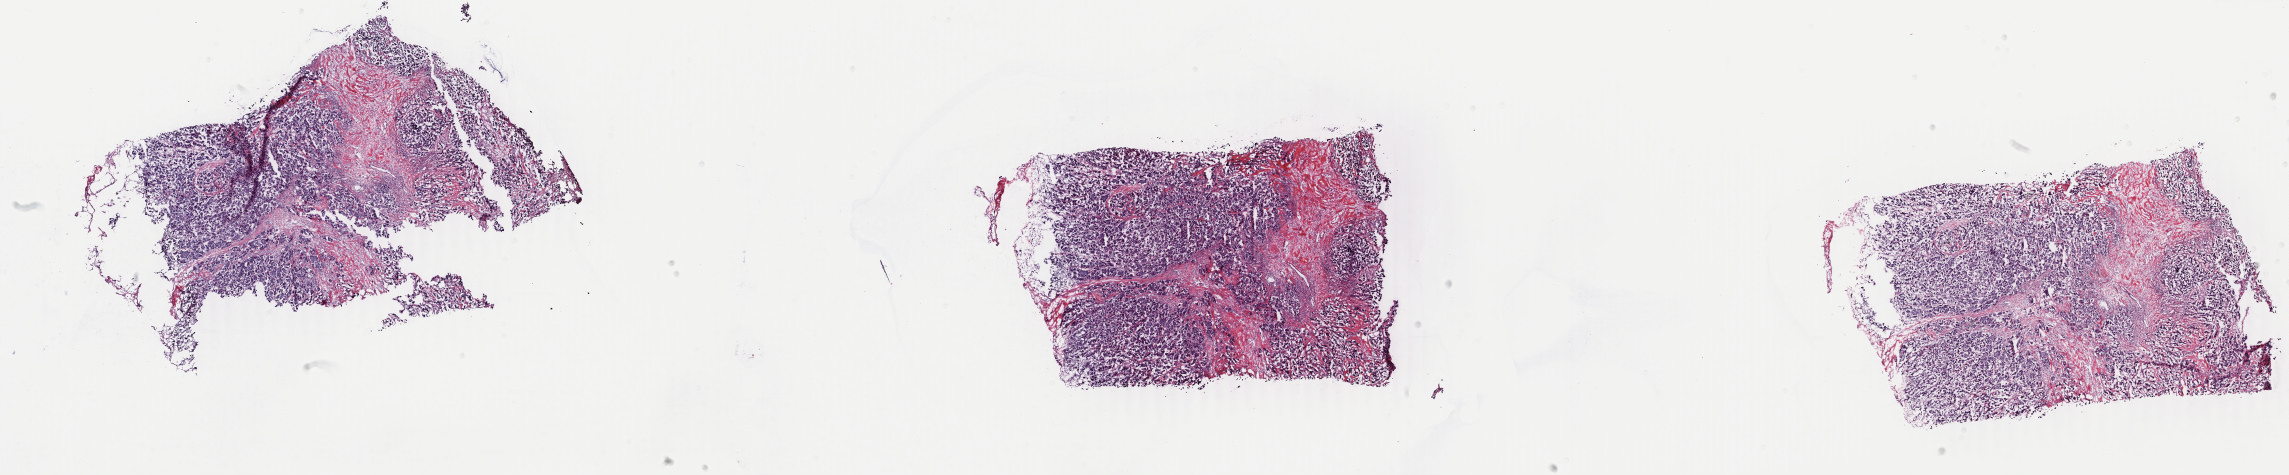
Hematoxylin and eosin (H&E) stained whole-slide image — shown as a low-resolution overview of the whole scanned area (about 36.4 x 7.6 mm, from a 40x scan), frozen section from the top of the tissue portion, primary tumour sample from the breast. Female patient; age at initial diagnosis 63 years. Composition of this section per pathologist review: tumour cells 90%, tumour nuclei 90%, normal cells 0%, stromal cells 10%, necrosis 0%. Infiltration values recorded for this section: lymphocyte infiltration 0%, monocyte infiltration 0%, neutrophil infiltration 0%.
AJCC pathologic stage: IIB. Lymph nodes positive (case pathology): 1 of 7 examined. Pathologic diagnosis: Infiltrating duct carcinoma, NOS.